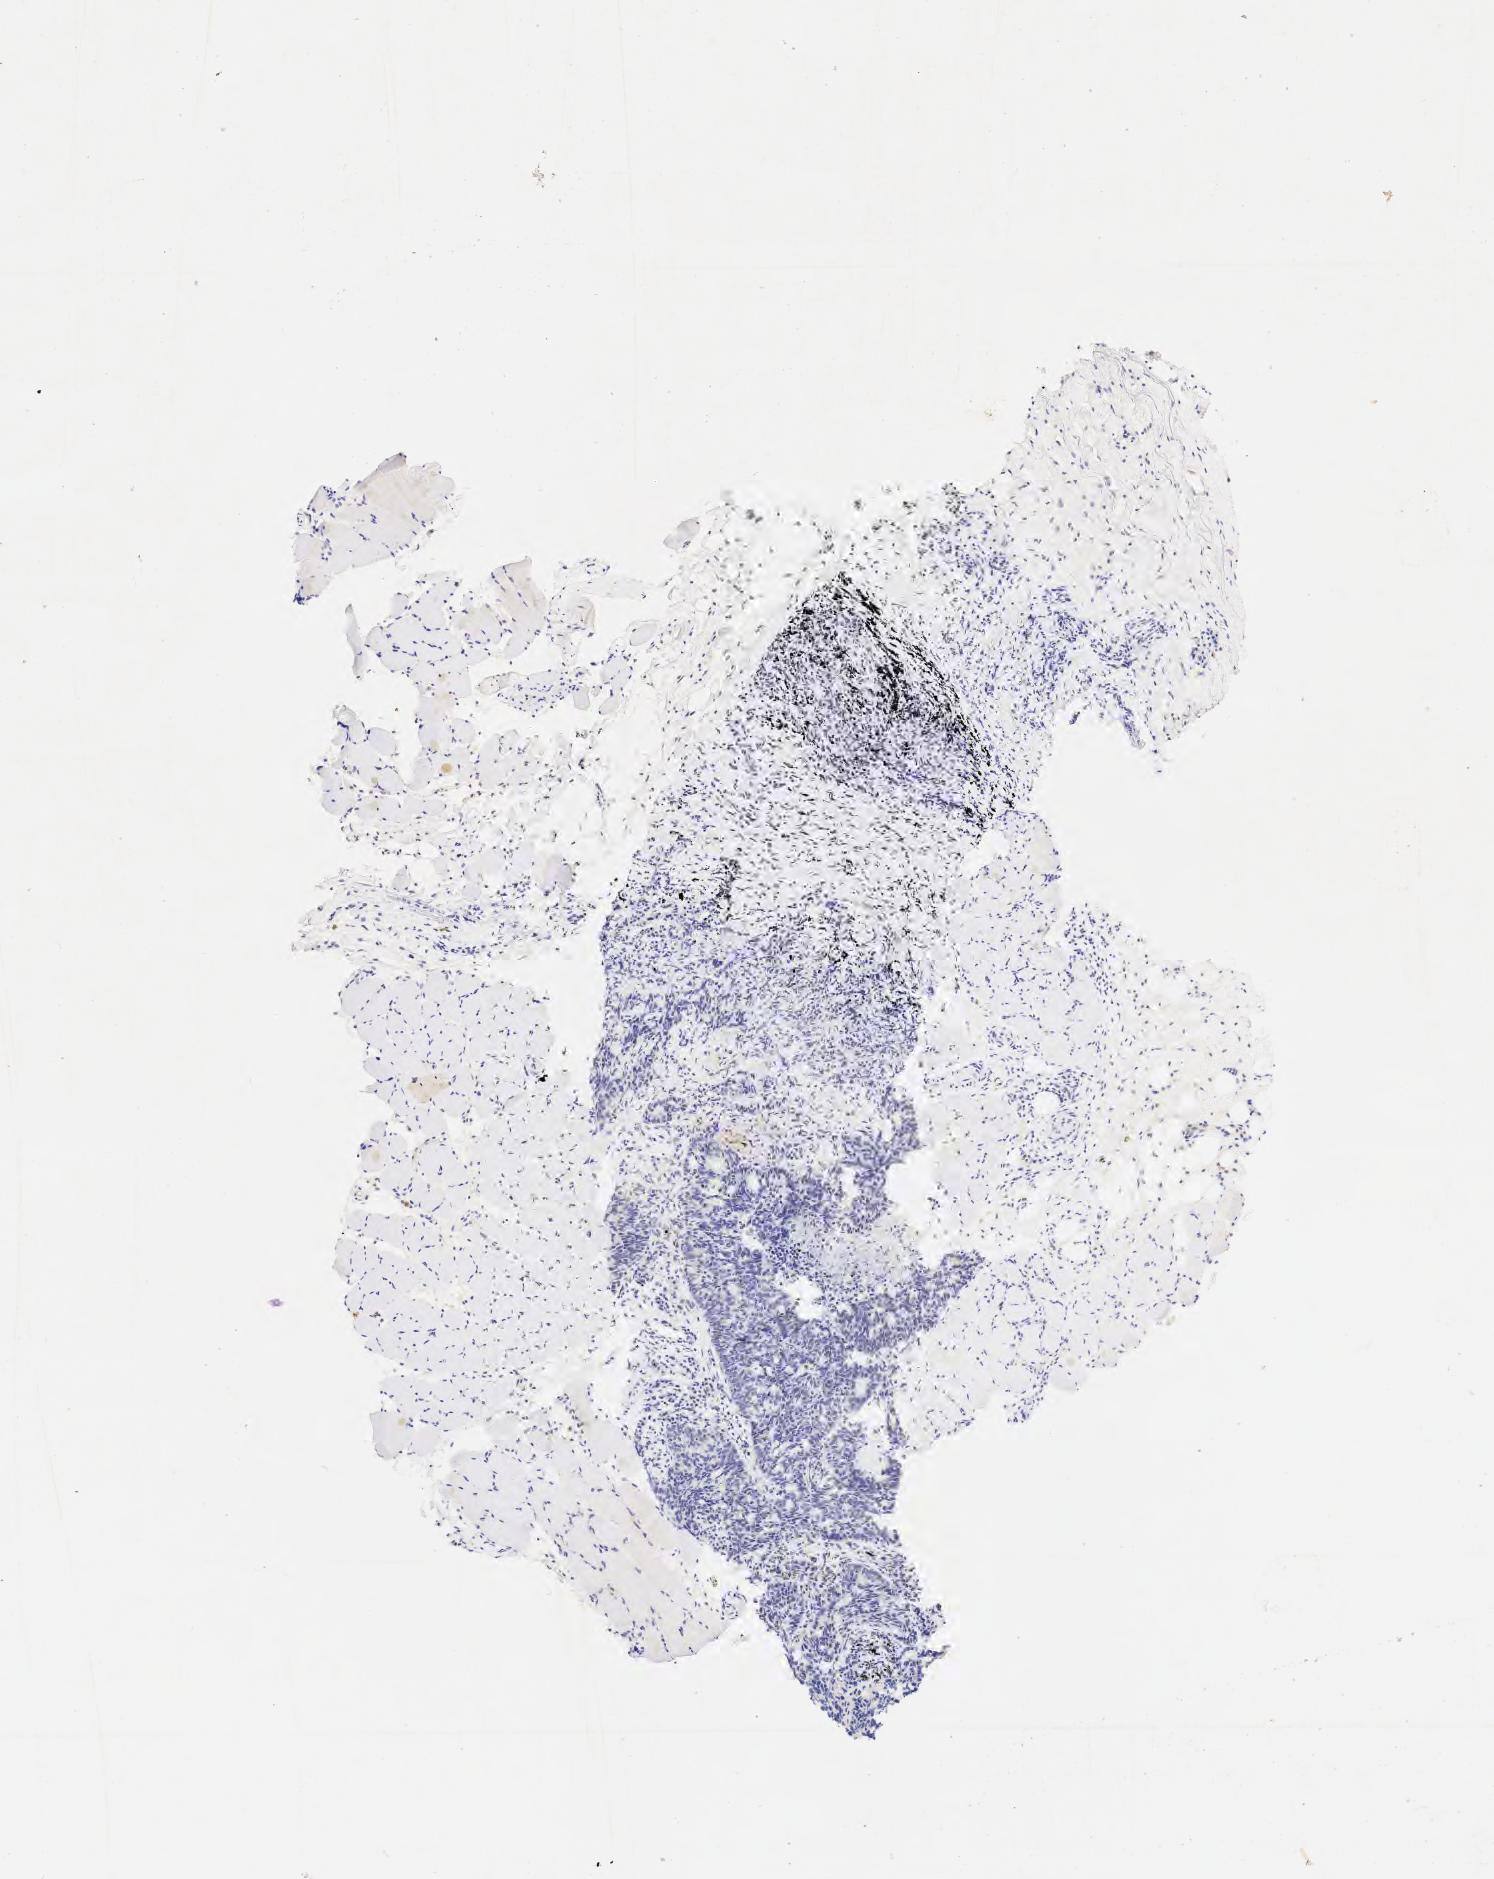
Immunohistochemistry (IHC) whole-slide image stained for TTF-1 (thyroid transcription factor 1) — shown as a low-resolution overview of the whole scanned area (about 3.0 x 3.8 mm). Tumor tissue. Site: lung (right). Patient female; 68 years old.
Diagnosis: Squamous cell carcinoma, large cell, nonkeratinizing, NOS.